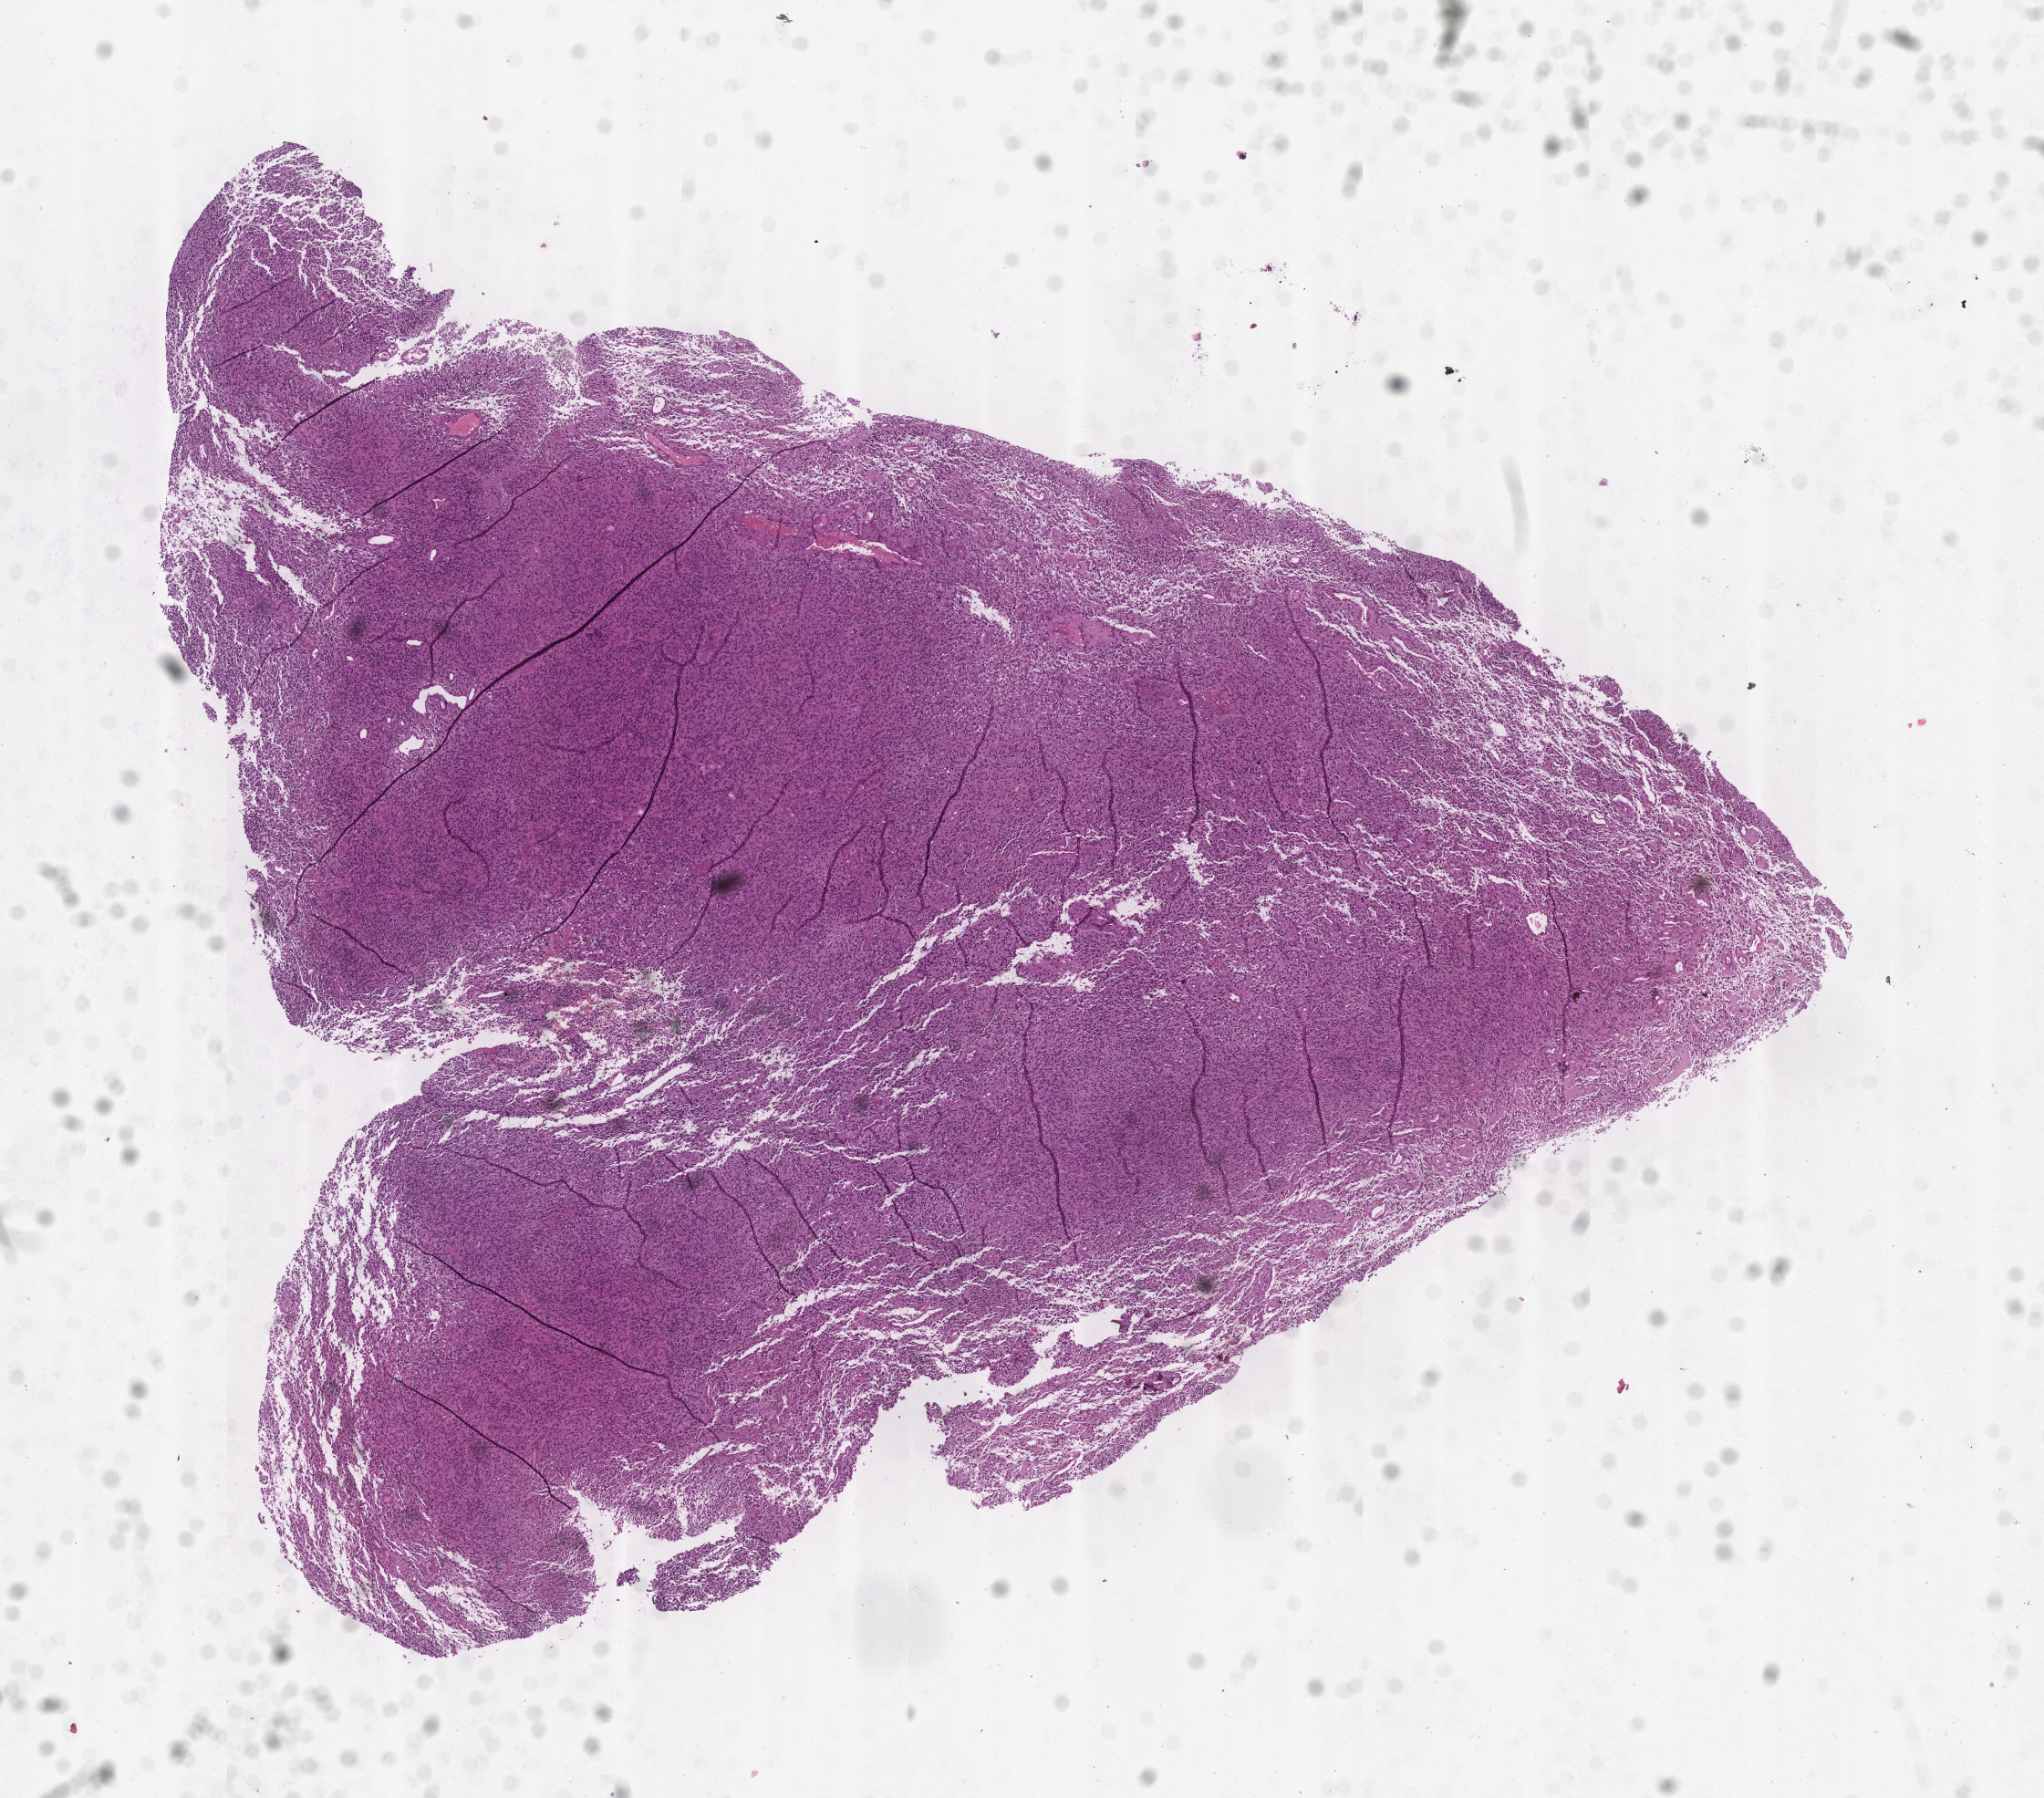
Whole-slide histology image, H&E-stained — whole scanned area (about 9.0 x 7.9 mm, slide scanned at 20x) shown as a low-resolution overview. Tumour tissue sample, sampled site: brain. Male, 71 y/o. Slide review estimates, as recorded: tumour nuclei 80%, necrosis 3%.
Diagnosis: Glioblastoma.